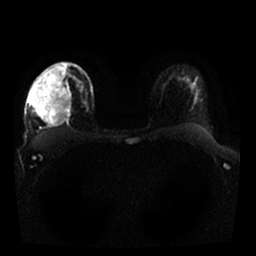
Breast MRI, one axial slice. Slice 14 of 25 in the series (ordered by position). Diffusion-weighted series; image 2 of 4 stored at this slice position (different b-values; order by instance number). 1.5 T. 4 mm slice thickness. 256 × 256 image matrix, field of view 330 × 330 mm. Female patient.
Outlined on this slice (expert manual segmentation):
- tumour on diffusion-weighted imaging: bounding box (x1, y1, x2, y2) in pixels: (66, 112, 71, 117)